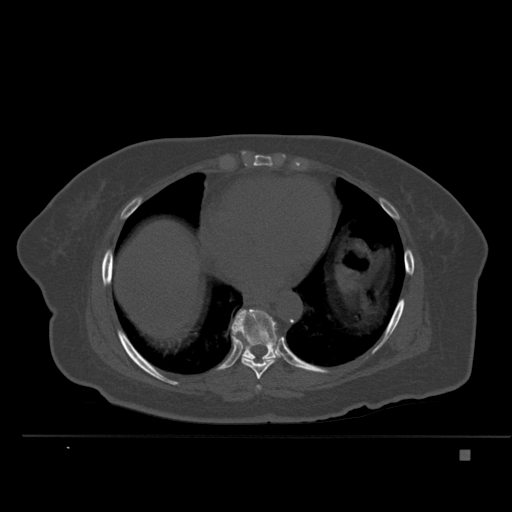
CT including the spine, one axial slice; position 306 of 477 along the scan axis; bone window (W 1800 / L 400 HU); 1.5 mm slice thickness; 512 × 512 image matrix, field of view 422 × 422 mm. Female patient, age 74 years. From the clinical record (not read from this slice): primary cancer: colon.
Annotated regions visible in this slice (semi-automatically segmented with operator editing):
- T7 vertebra: bounding box [x1, y1, x2, y2] px = [256, 385, 261, 390]
- T8 vertebra: [233, 334, 278, 379]
- T9 vertebra: [232, 309, 279, 361]